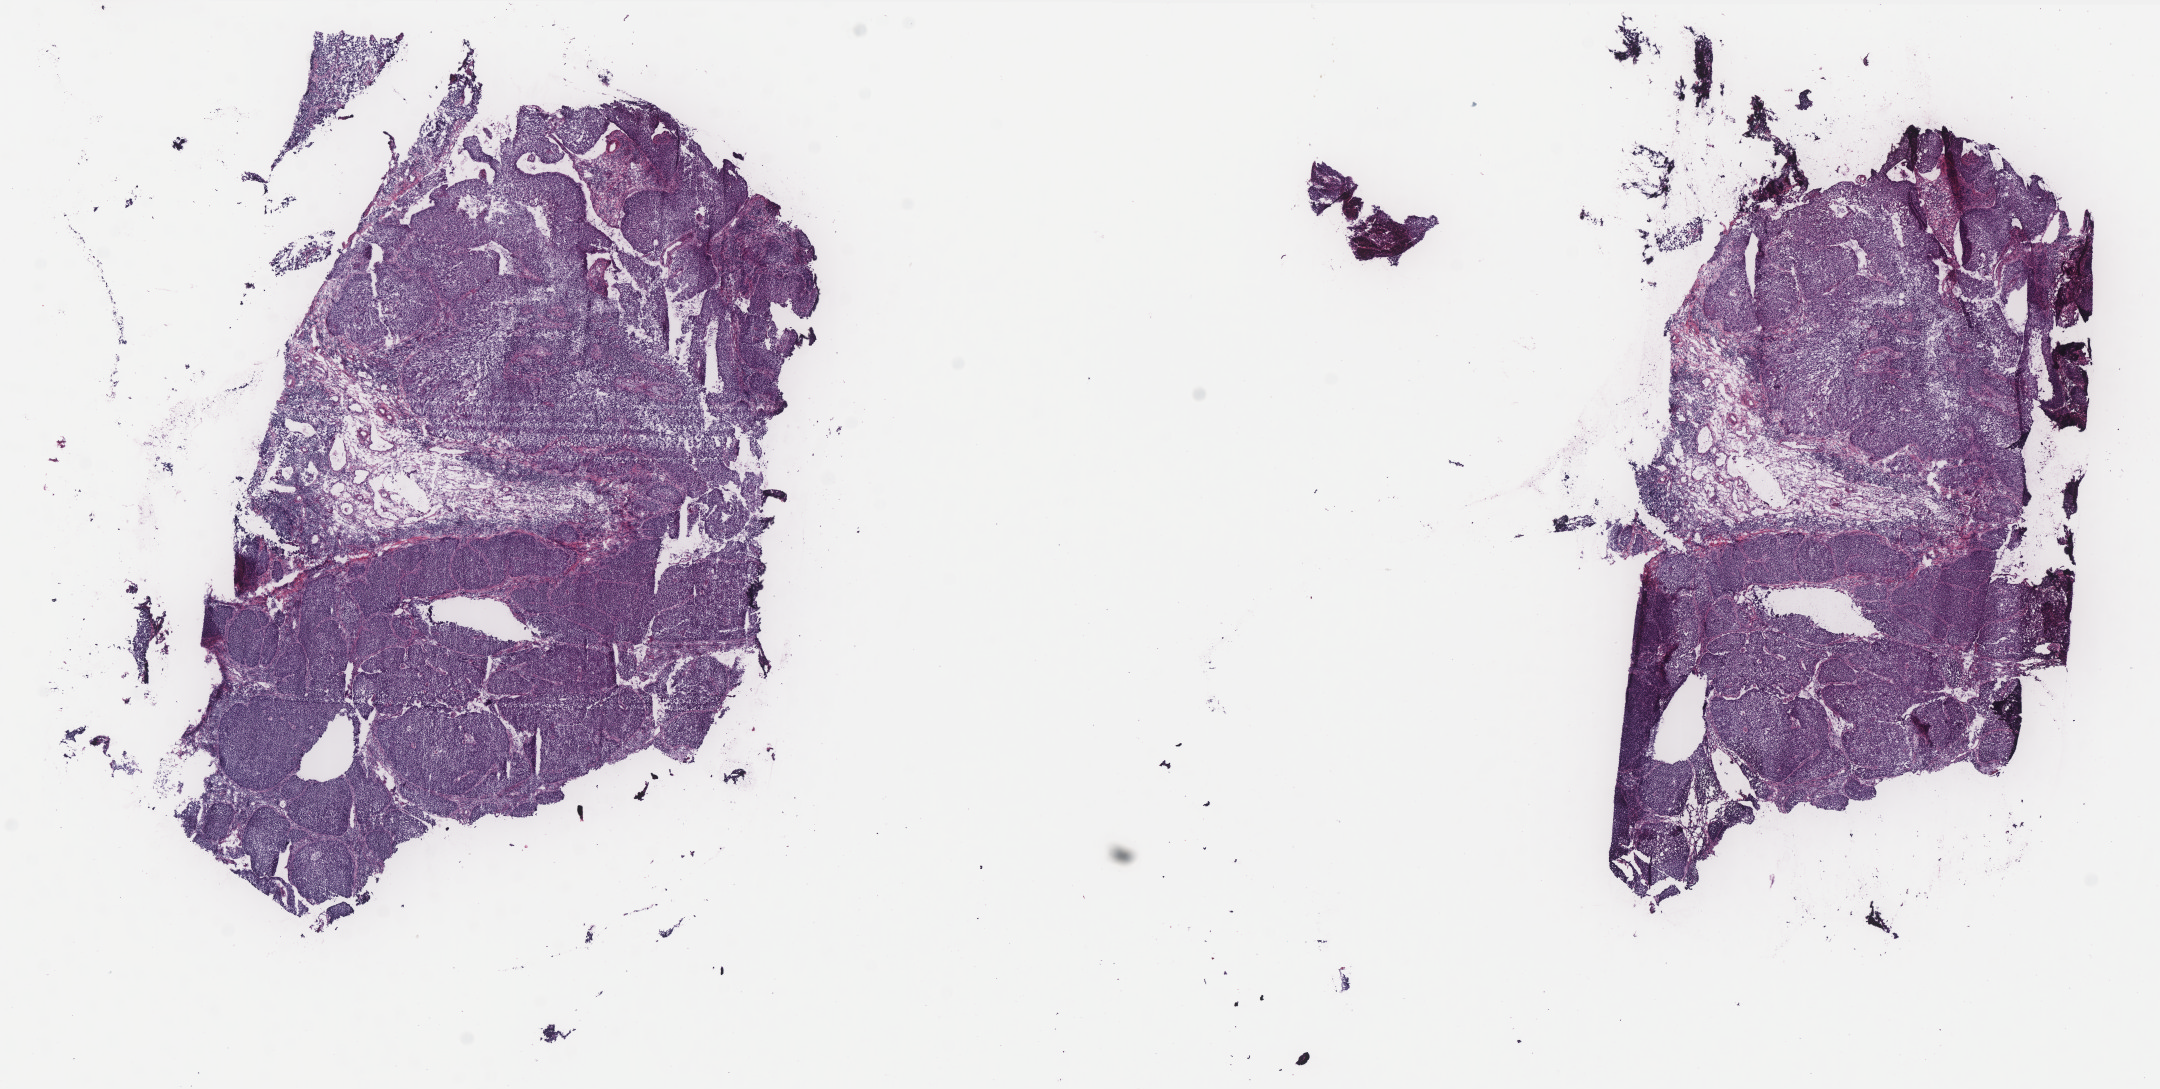
Digitized H&E tissue section (whole slide), low-resolution overview of the scanned area, about 17.3 x 8.7 mm (slide scanned at 40x), frozen section from the top of the tissue portion, sample: primary tumour, cervix. Female, age 25 years at initial diagnosis. Histologic grade: G2 (moderately differentiated). Composition of this section per pathologist review: tumour cells 100%, tumour nuclei 75%, normal cells 0%, stromal cells 0%, necrosis 0%. Inflammatory infiltration, as recorded: lymphocyte infiltration 0%, monocyte infiltration 0%, neutrophil infiltration 0%.
Lymph nodes positive (case pathology): 0 of 8 examined. Pathologic diagnosis: Squamous cell carcinoma, NOS.